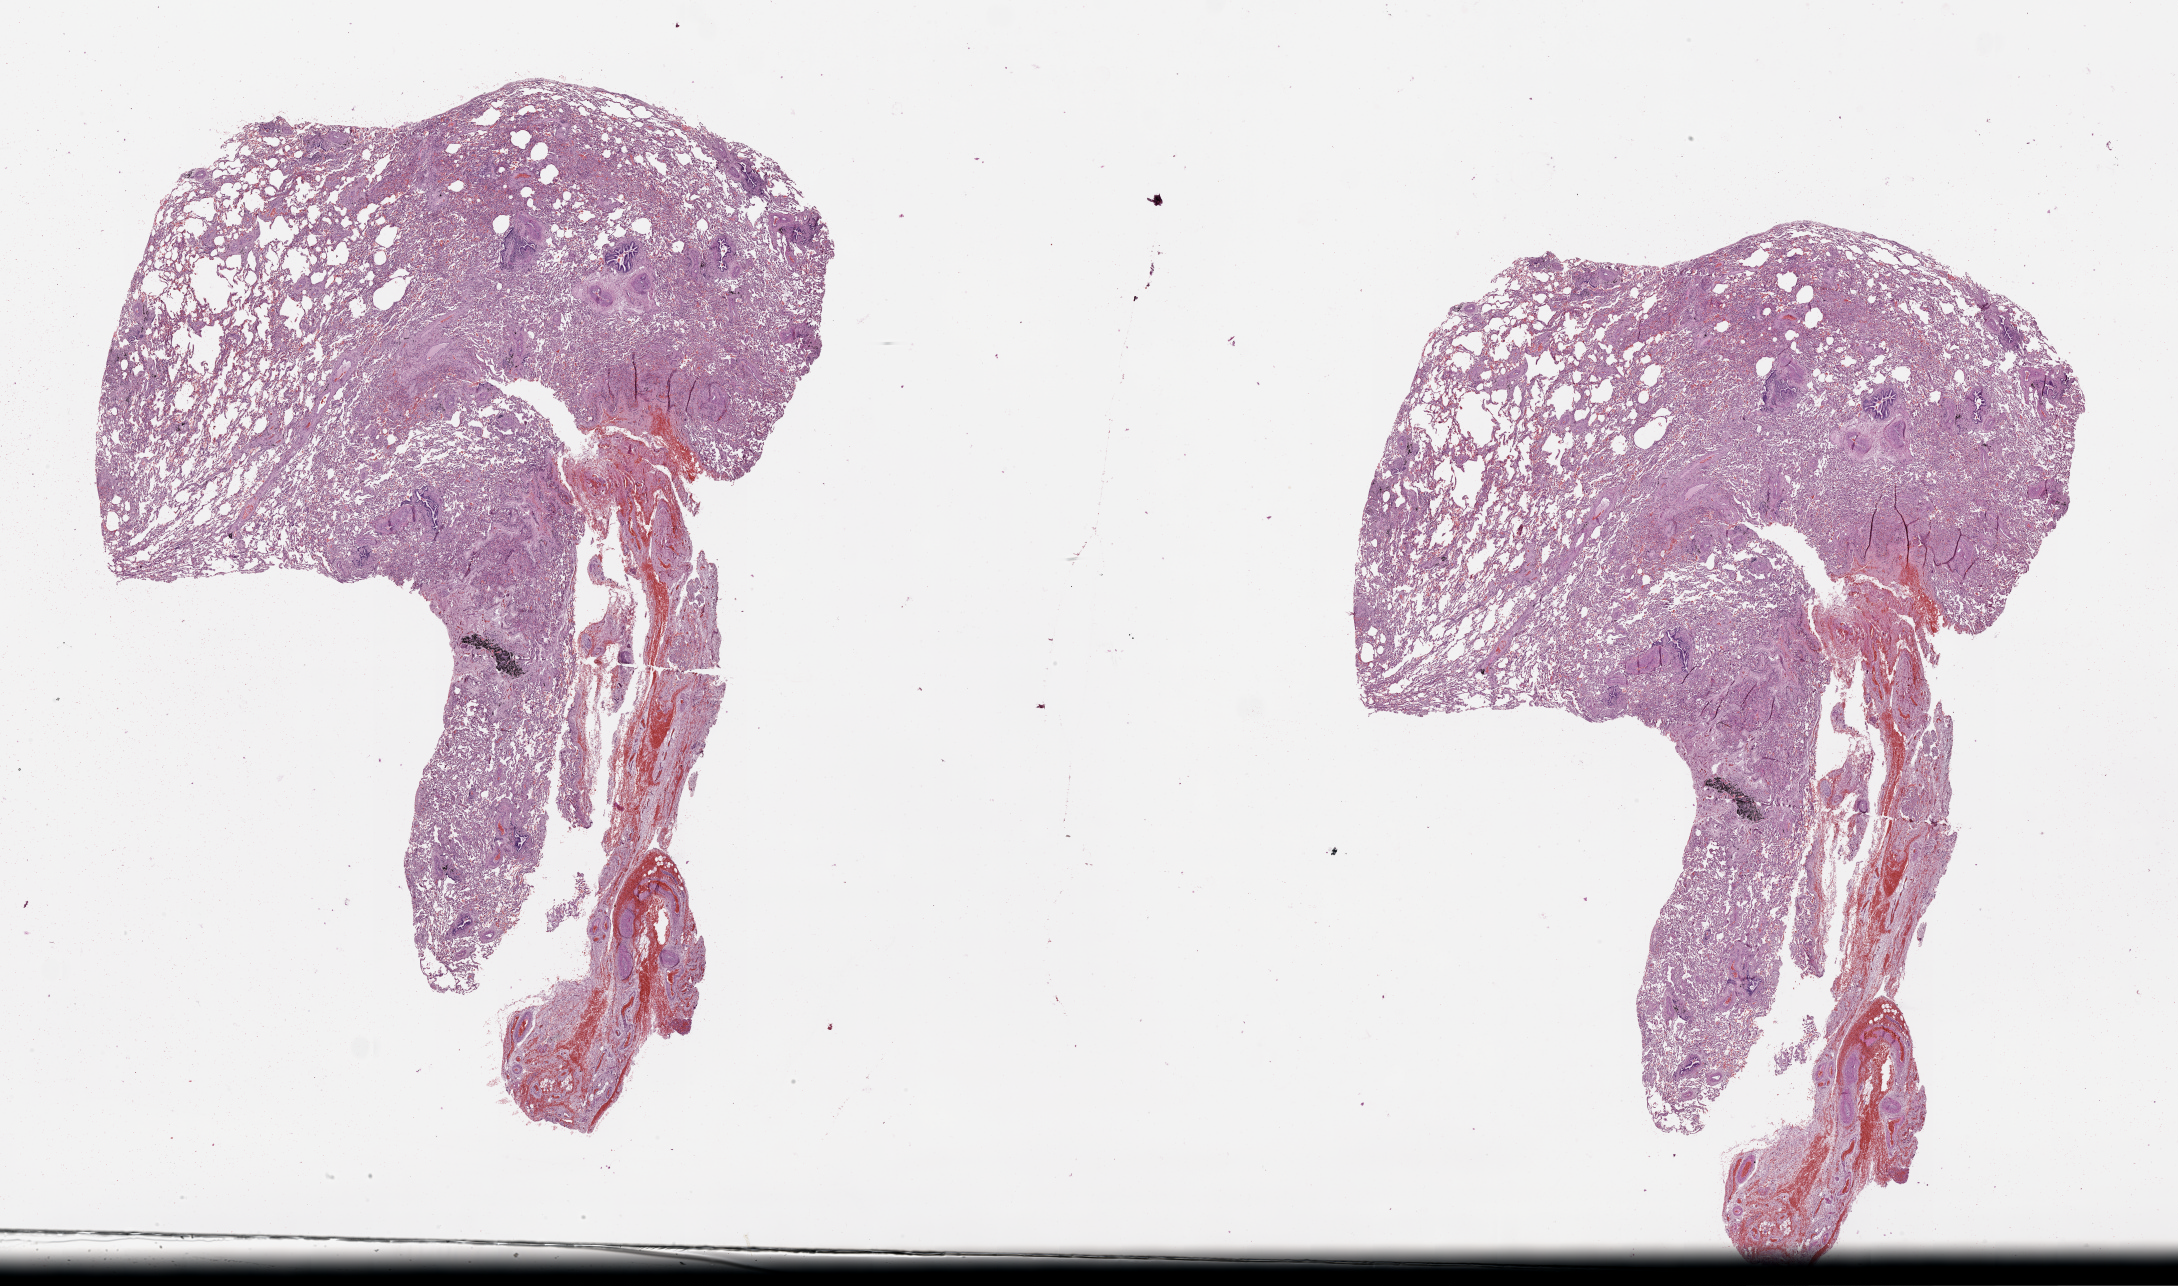
Hematoxylin and eosin (H&E) stained whole-slide image — shown as a low-resolution overview of the whole scanned area (about 35.1 x 20.7 mm); lung, normal (non-tumour) tissue. 63-year-old female patient.
This section: normal (non-tumour) tissue from the same patient. Patient diagnosis (cohort enrolment): squamous cell carcinoma (lung).